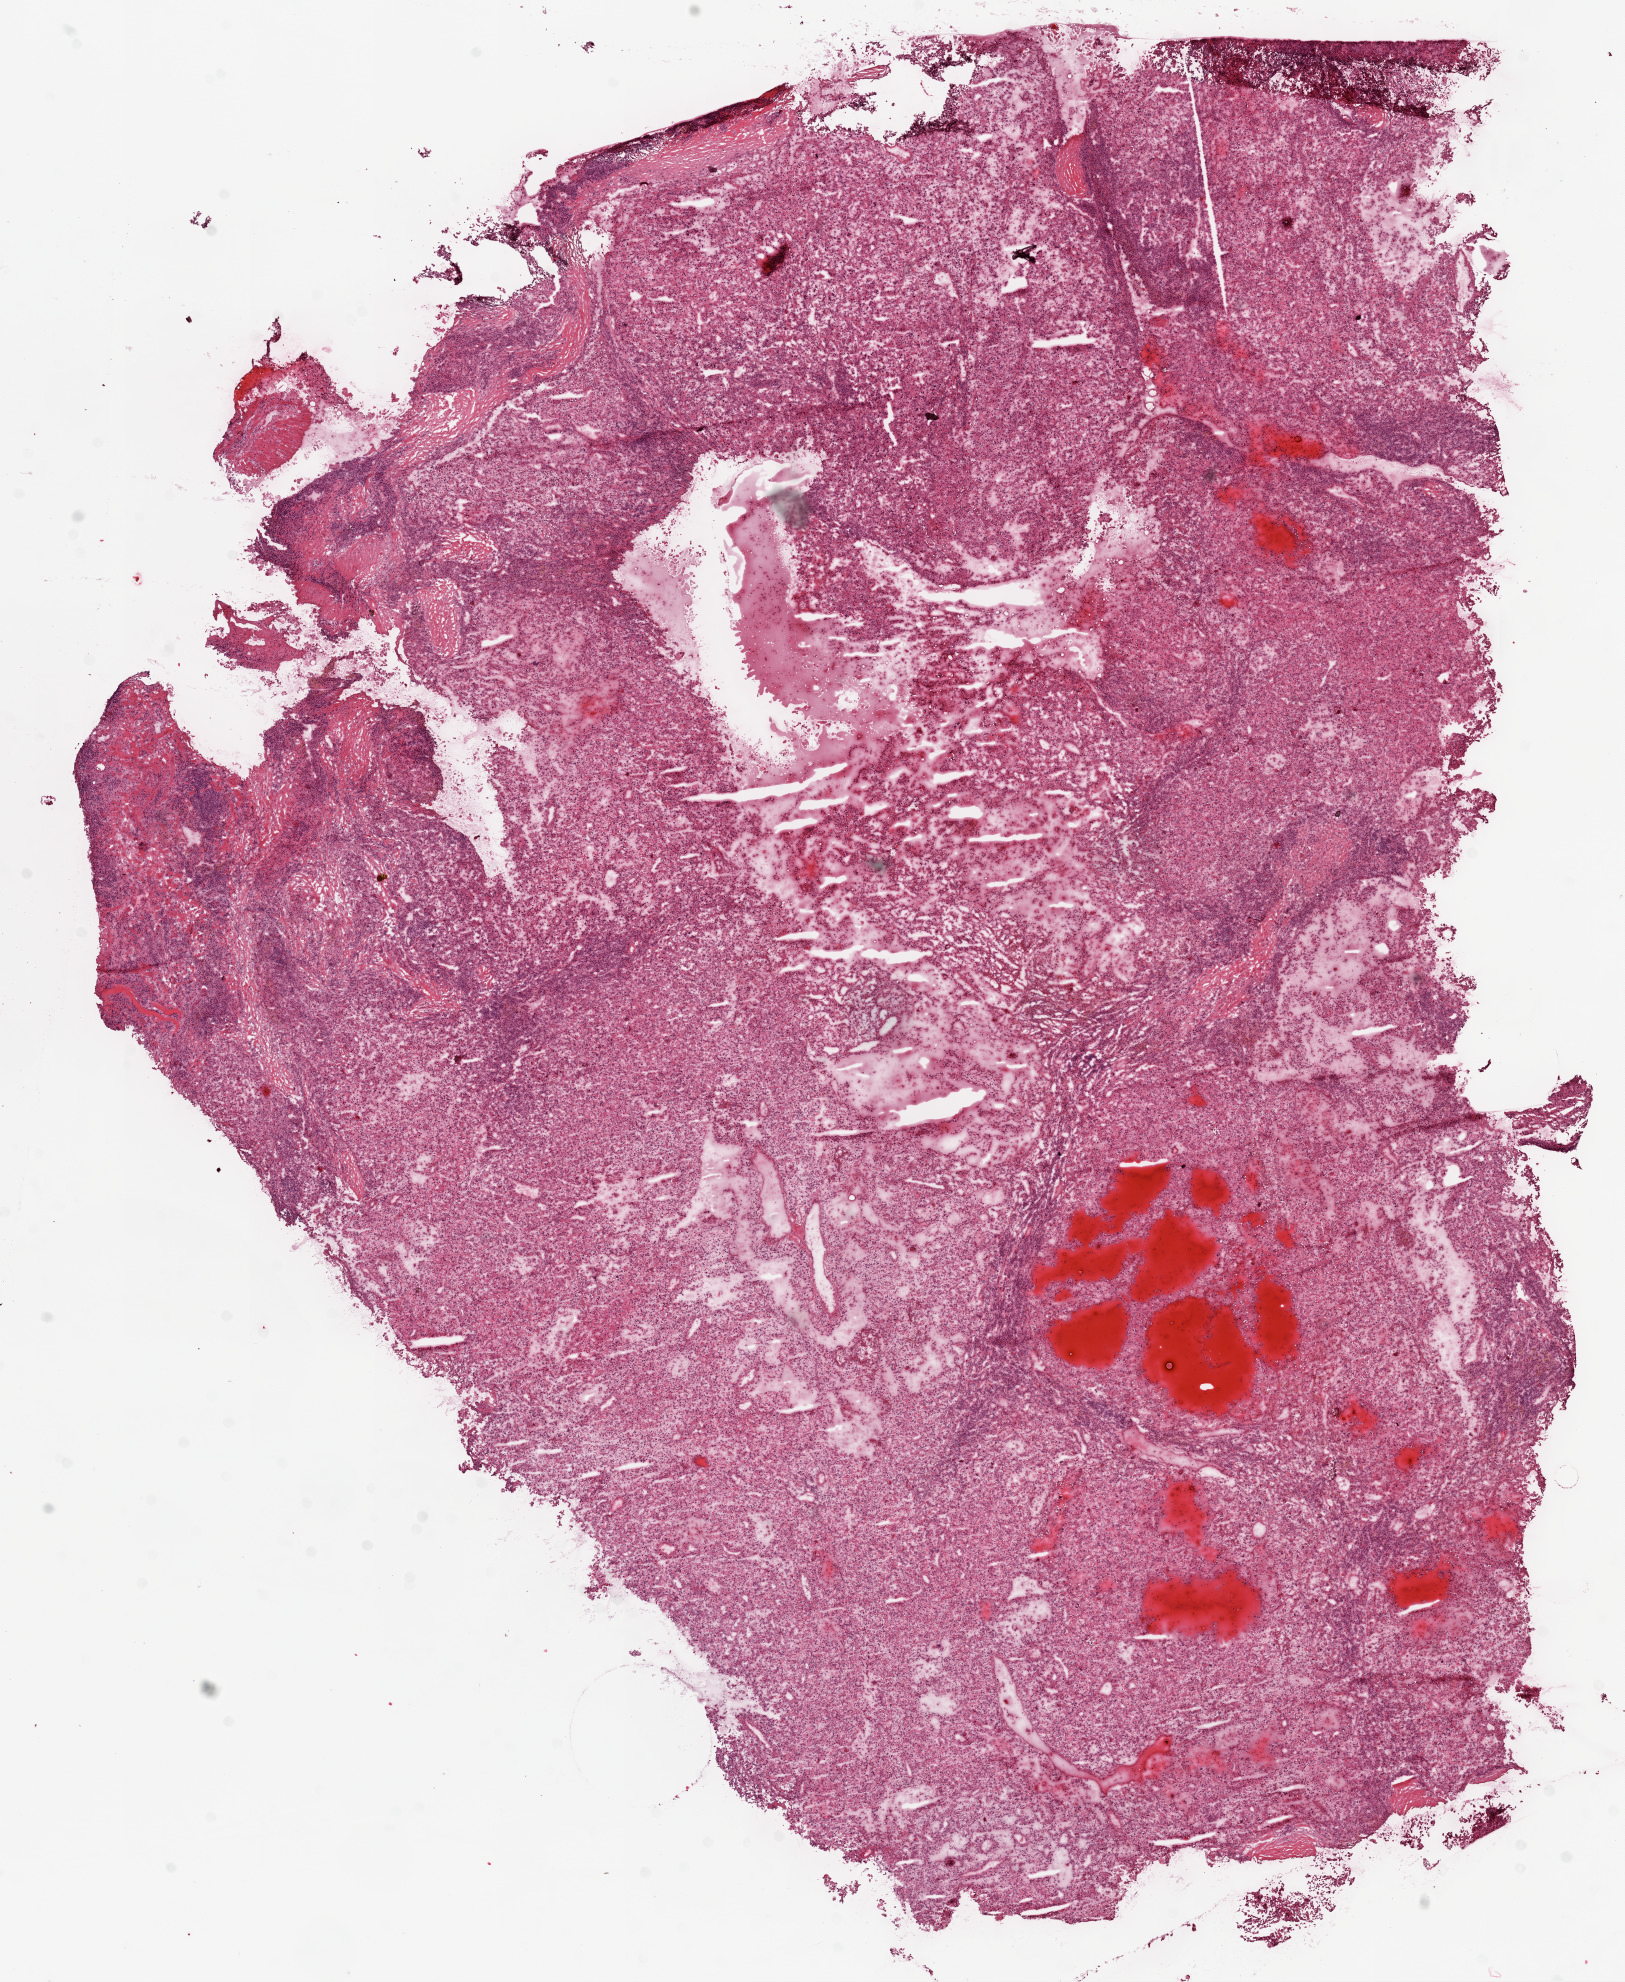
Digitized H&E tissue section (whole slide) — a low-resolution overview of the entire scanned area, about 13.0 x 15.9 mm (slide scanned at 20x). Frozen section from the top of the tissue portion. Sample: primary tumour, kidney. Patient: male, age at initial diagnosis 70 years.
Histologic diagnosis: Clear cell adenocarcinoma, NOS.